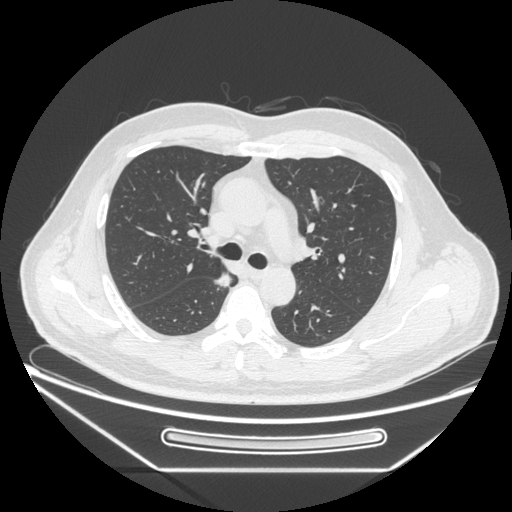
Chest CT, one axial slice; slice 165 of 271 in the series (ordered by position); 120 kVp; lung window (W 1500 / L -600 HU); 1.25 mm slice thickness; 512 × 512 image matrix, field of view 414 × 414 mm. Male patient, age 49 years. Case-level facts recorded for this patient, not image findings: clinical TNM (as recorded): T1b N0 M0.
Structures marked on this image (bounding box drawn by a radiologist):
- lung tumour (recorded histology: adenocarcinoma): box from (x=210, y=266) to (x=237, y=297) px